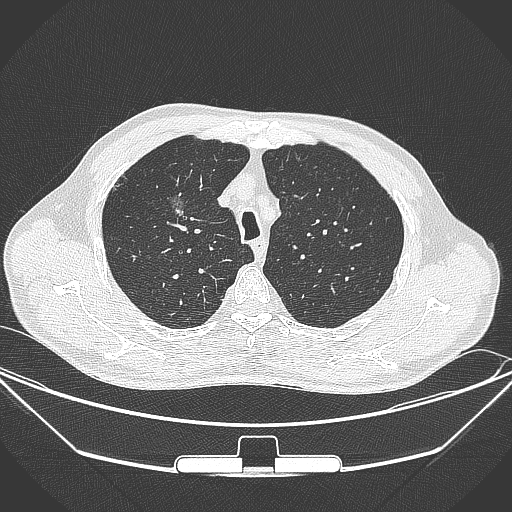
Chest CT, one axial slice. 120 kVp. Lung window (W 1500 / L -600 HU). 1 mm slice thickness. 512 × 512 image matrix, field of view 399 × 399 mm. Male patient, age 67 years. From the clinical record (not read from this slice): clinical TNM (as recorded): T1c N0 M0; histopathological grade: G2.
Structures marked on this image (bounding box drawn by a radiologist):
- lung tumour (recorded histology: adenocarcinoma): bounding box (x1, y1, x2, y2) in pixels: (155, 183, 194, 233)